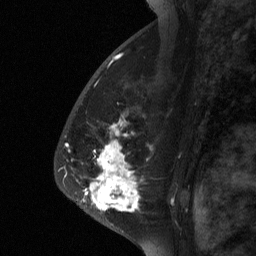
Breast MRI (dynamic contrast-enhanced), one sagittal slice. Slice 42 of 64 in the series (ordered by position). Dynamic contrast-enhanced study with each time point stored as its own series, time point 2 of 3 at this slice position (early post-contrast, ordered by acquisition time). 1.5 T. TE 4.8 ms, TR 27 ms. 2 mm slice thickness. 256 × 256 image matrix. Female patient, age 56 years. Case-level facts recorded for this patient, not image findings: setting: breast cancer imaged before/during neoadjuvant chemotherapy; receptor status: HER2-positive.
Annotated regions visible in this slice (semi-automatic segmentation, software-assisted and operator-edited):
- analysis volume of interest (the breast-tissue region the enhancement analysis was run in; not a lesion): bounding box (x1, y1, x2, y2) in pixels: (72, 104, 182, 229)
- tumour enhancement mask (voxels above the 90 % enhancement threshold inside the analysis volume of interest): (82, 124, 139, 212)